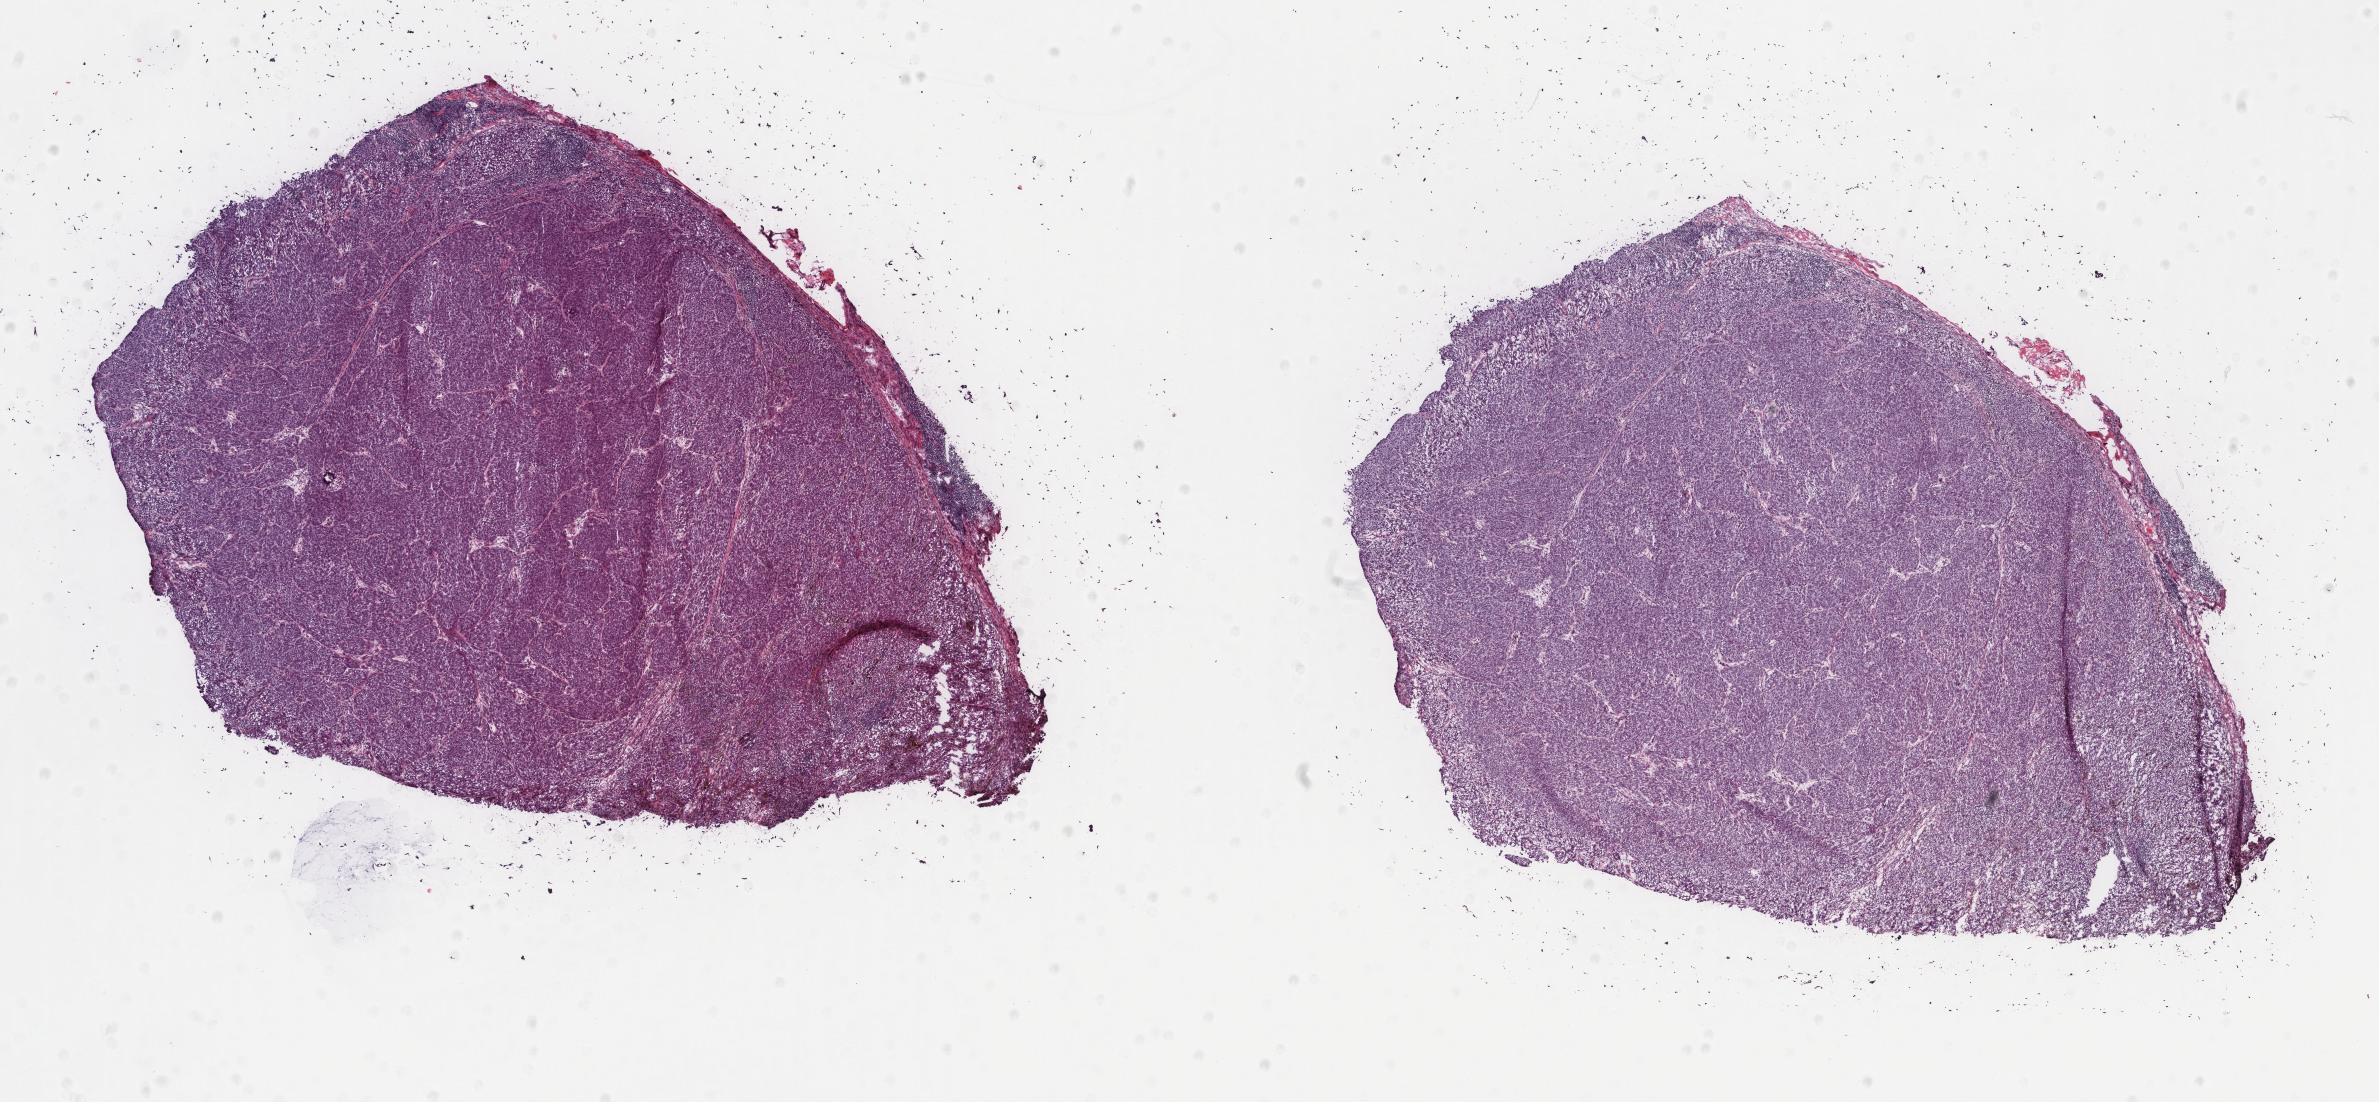
Digitized Hematoxylin and eosin (H&E) stained tissue section (whole slide), a low-resolution overview of the entire scanned area, about 18.9 x 8.7 mm (from a 40x scan), frozen section from the top of the tissue portion, metastatic tumour sample, sampled site: skin. Female, age 65 years at initial diagnosis.
This section: metastatic tumour tissue. Patient diagnosis: Malignant melanoma, NOS.